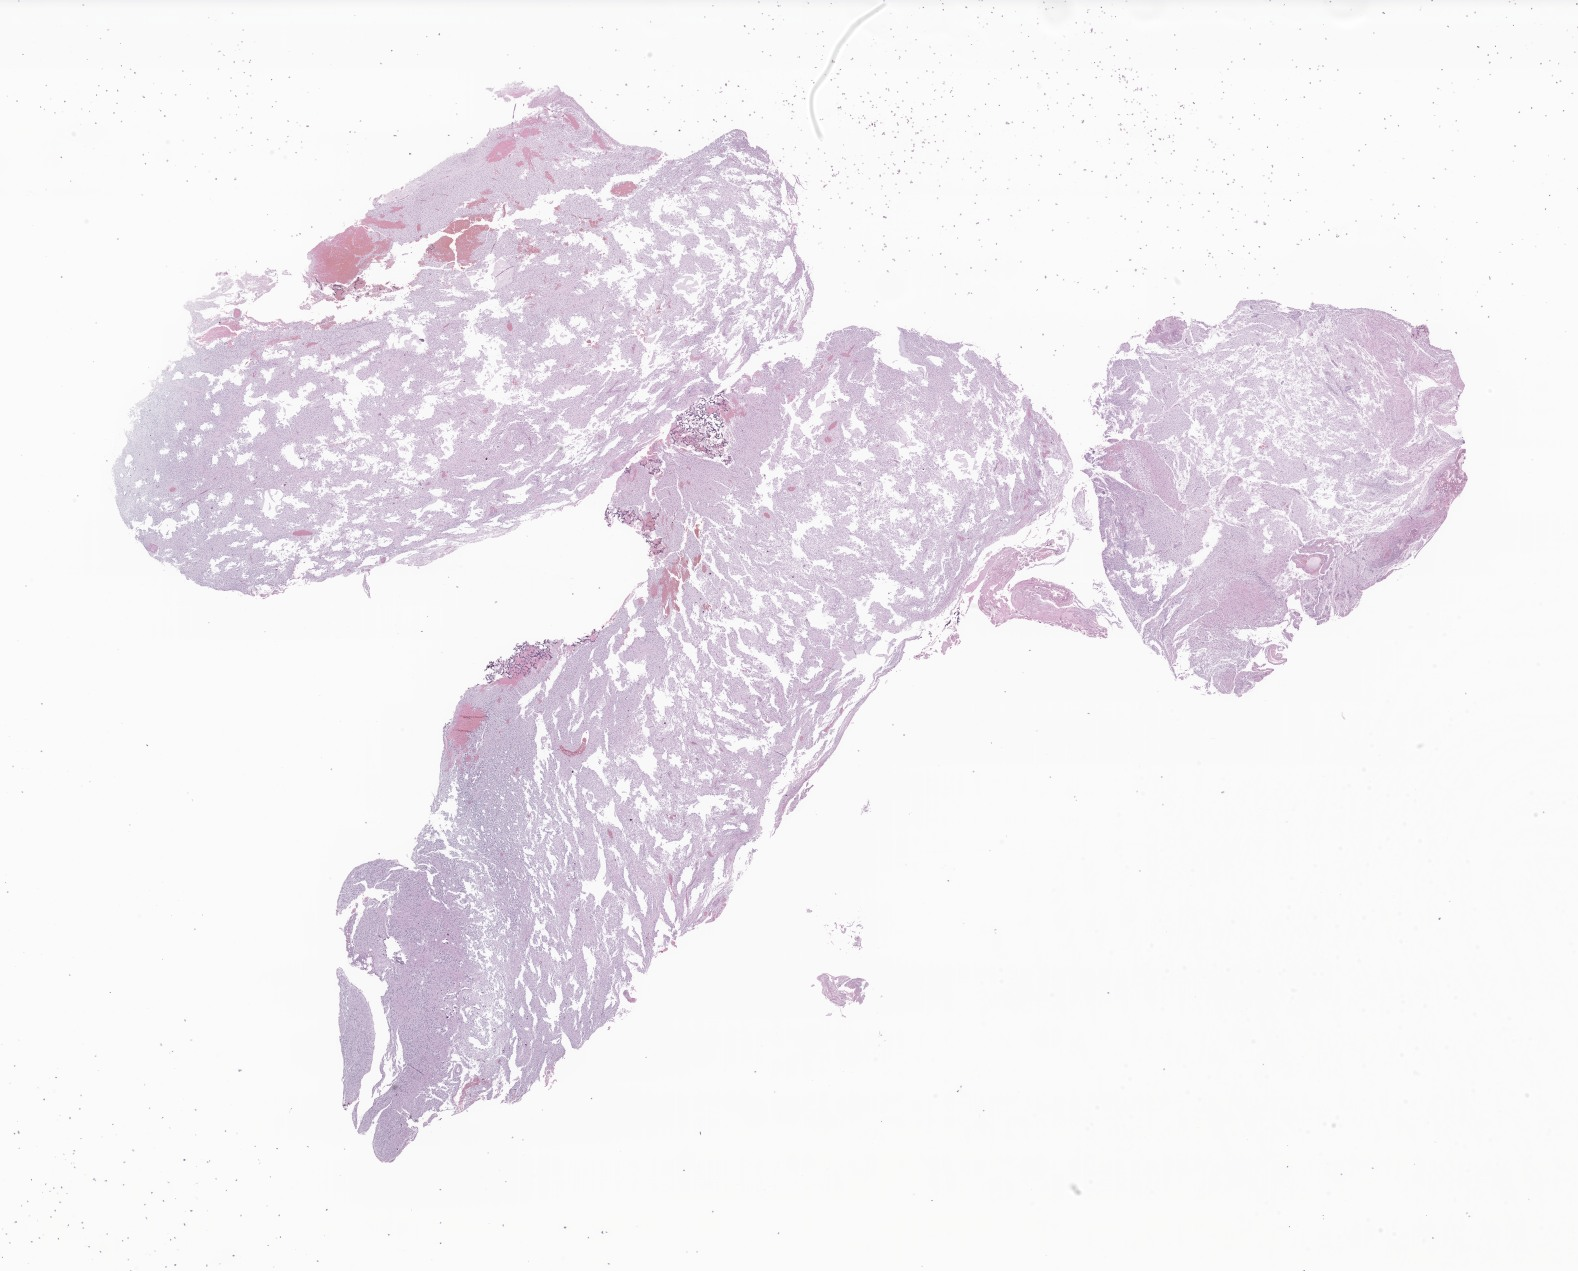
H&E whole-slide image of tumor tissue from the brain — shown as a low-resolution overview of the whole scanned area (about 26.6 x 21.4 mm), formalin-fixed paraffin-embedded section. Patient male; age 60 months (5 years).
Diagnosis (ICD-O-3 morphology term): Pilocytic astrocytoma.